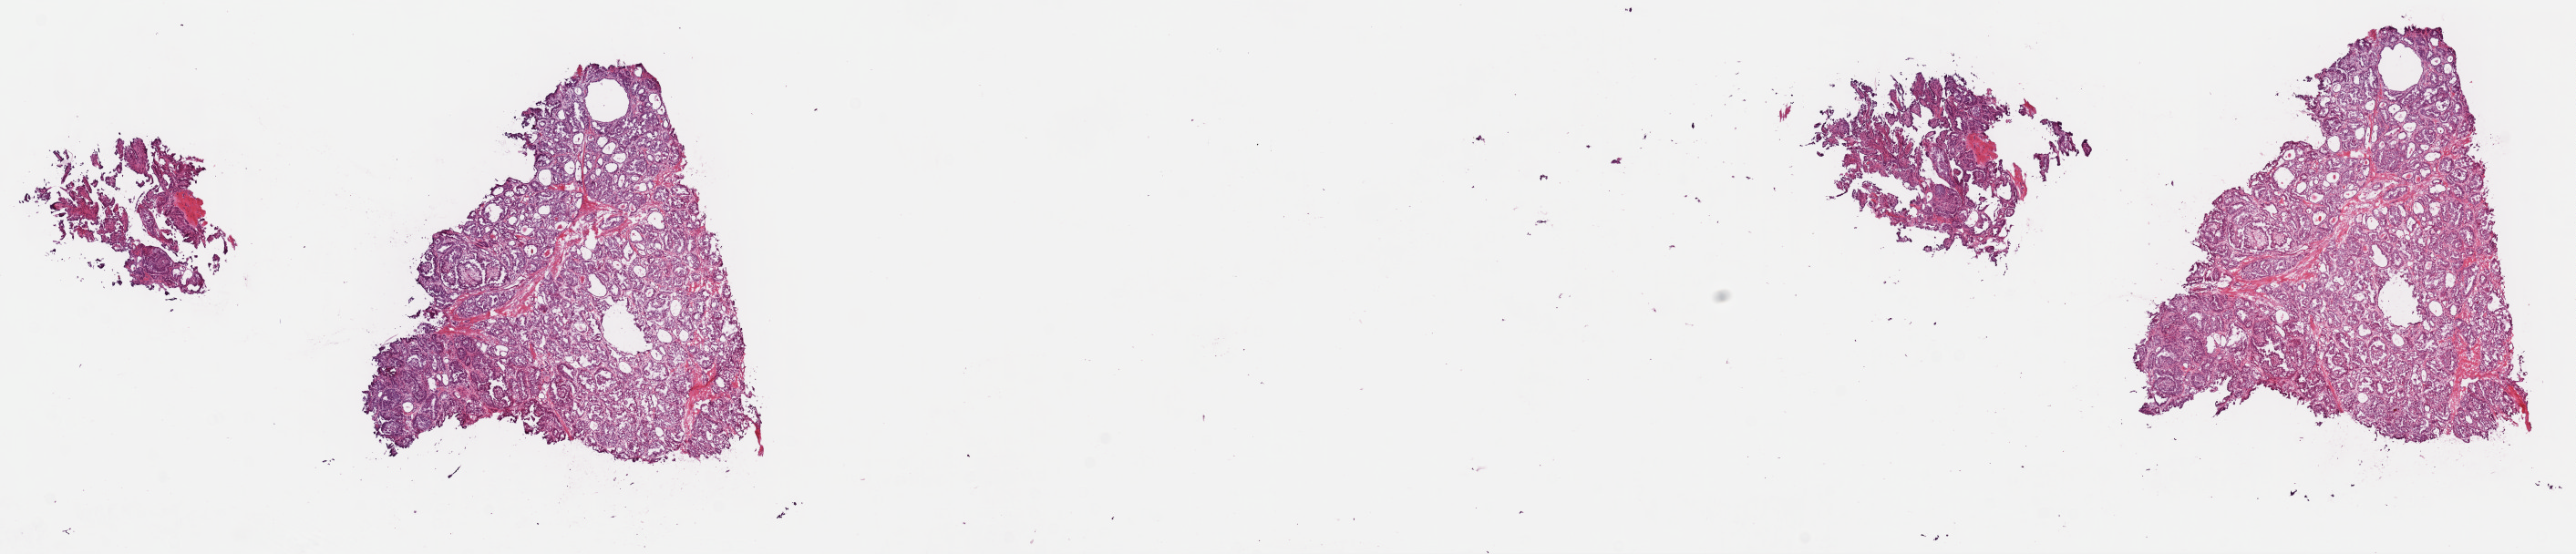
Whole-slide histology image, Hematoxylin and eosin (H&E) stained — low-resolution overview of the scanned area, about 22.3 x 4.8 mm (acquisition: 40x scan). Frozen section from the top of the tissue portion. Thyroid, primary tumour sample. Male patient; age at initial diagnosis 46 years. Slide review estimates, as recorded: tumour cells 85%, tumour nuclei 85%, normal cells 0%, stromal cells 15%, necrosis 0%. Inflammatory infiltration, as recorded: lymphocyte infiltration 1%, monocyte infiltration 0%, neutrophil infiltration 0%.
TNM: T1b N1b MX. AJCC pathologic stage: IVA. Histologic diagnosis: Papillary adenocarcinoma, NOS.